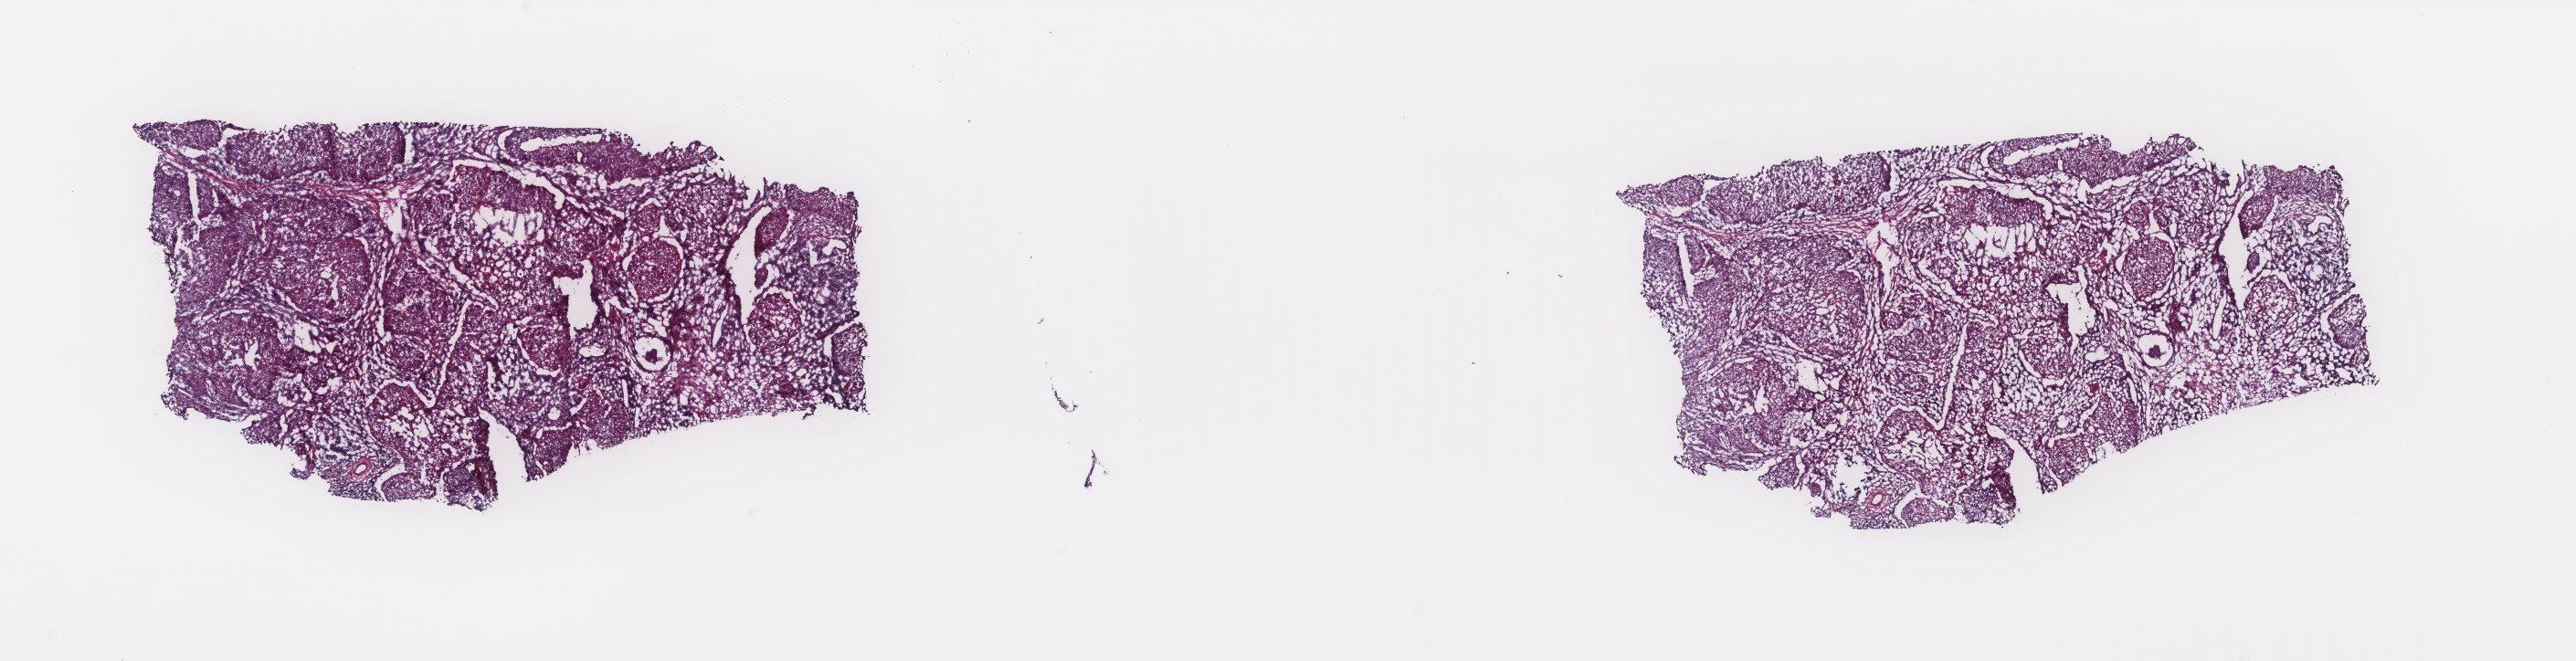
Hematoxylin and eosin (H&E) stained whole-slide image, a low-resolution overview of the entire scanned area, about 22.6 x 5.8 mm (from a 40x scan). Frozen section from the top of the tissue portion. Primary tumour sample from the cervix. Female patient; age at initial diagnosis 36 years. Histologic grade: G2 (moderately differentiated). Pathologist review of this section (percent, as recorded): tumour cells 70%, tumour nuclei 70%, normal cells 0%, stromal cells 30%, necrosis 0%. Inflammatory infiltration, as recorded: lymphocyte infiltration 50%, monocyte infiltration 0%, neutrophil infiltration 5%.
FIGO stage: IB. Histologic diagnosis: Squamous cell carcinoma, NOS (cervix uteri).